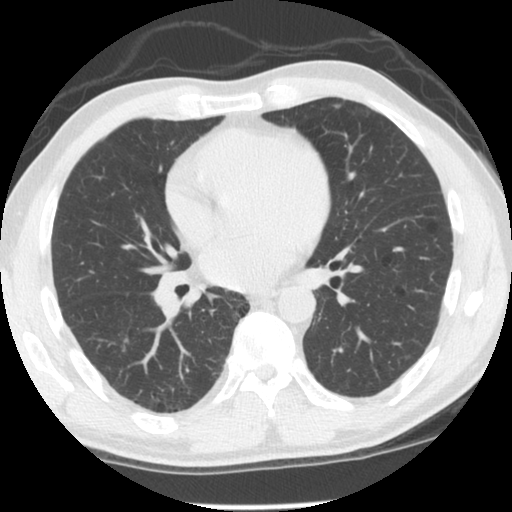
Chest CT (low-dose screening protocol), one axial image; first (baseline) screen; lung window (W 1500 / L -600 HU); 2.5 mm slice thickness; 140 kVp; slice 54 of 125 in the series; 512 × 512 image matrix. Male, age 60 years at enrolment.
- Expert reader's lesion annotation, box from (x=90, y=320) to (x=142, y=368) px.
- The exam's reader record, not a measurement of the box and not confirmed to be the same lesion: non-calcified nodule or mass ≥4 mm, right lower lobe, 9 × 7 mm, spiculated (stellate) margins.
- Official screen result: positive, change unspecified: nodule(s) >= 4 mm or enlarging nodule(s), mass(es), or other non-specific abnormalities suspicious for lung cancer.
- Later outcome: lung cancer diagnosed 534 days after this screen — adenocarcinoma, NOS, right lower lobe, stage IA (AJCC 6th edition), 18 mm at pathology.